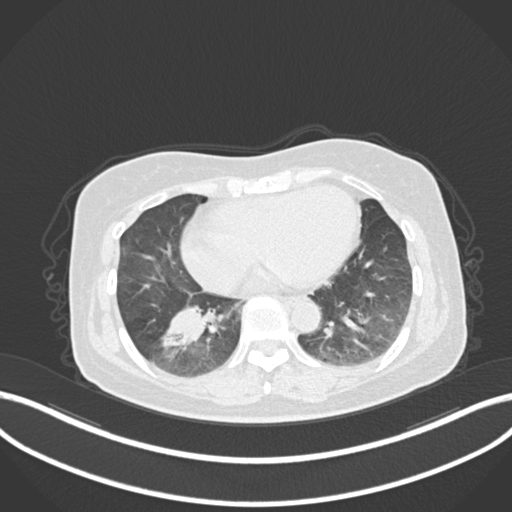
Chest CT, one axial slice; position 47 of 222 along the scan axis; 120 kVp; lung window (W 1500 / L -600 HU); 1 mm slice thickness; 512 × 512 image matrix, field of view 400 × 400 mm. Patient: female, 67 years. Case-level facts recorded for this patient, not image findings: clinical TNM (as recorded): T1c N1 M0; histopathological grade: G2-3.
Outlined on this slice (rectangle marked by the reading radiologist):
- lung tumour (recorded histology: adenocarcinoma): bounding box <158,298,212,350> (left, top, right, bottom; pixels)